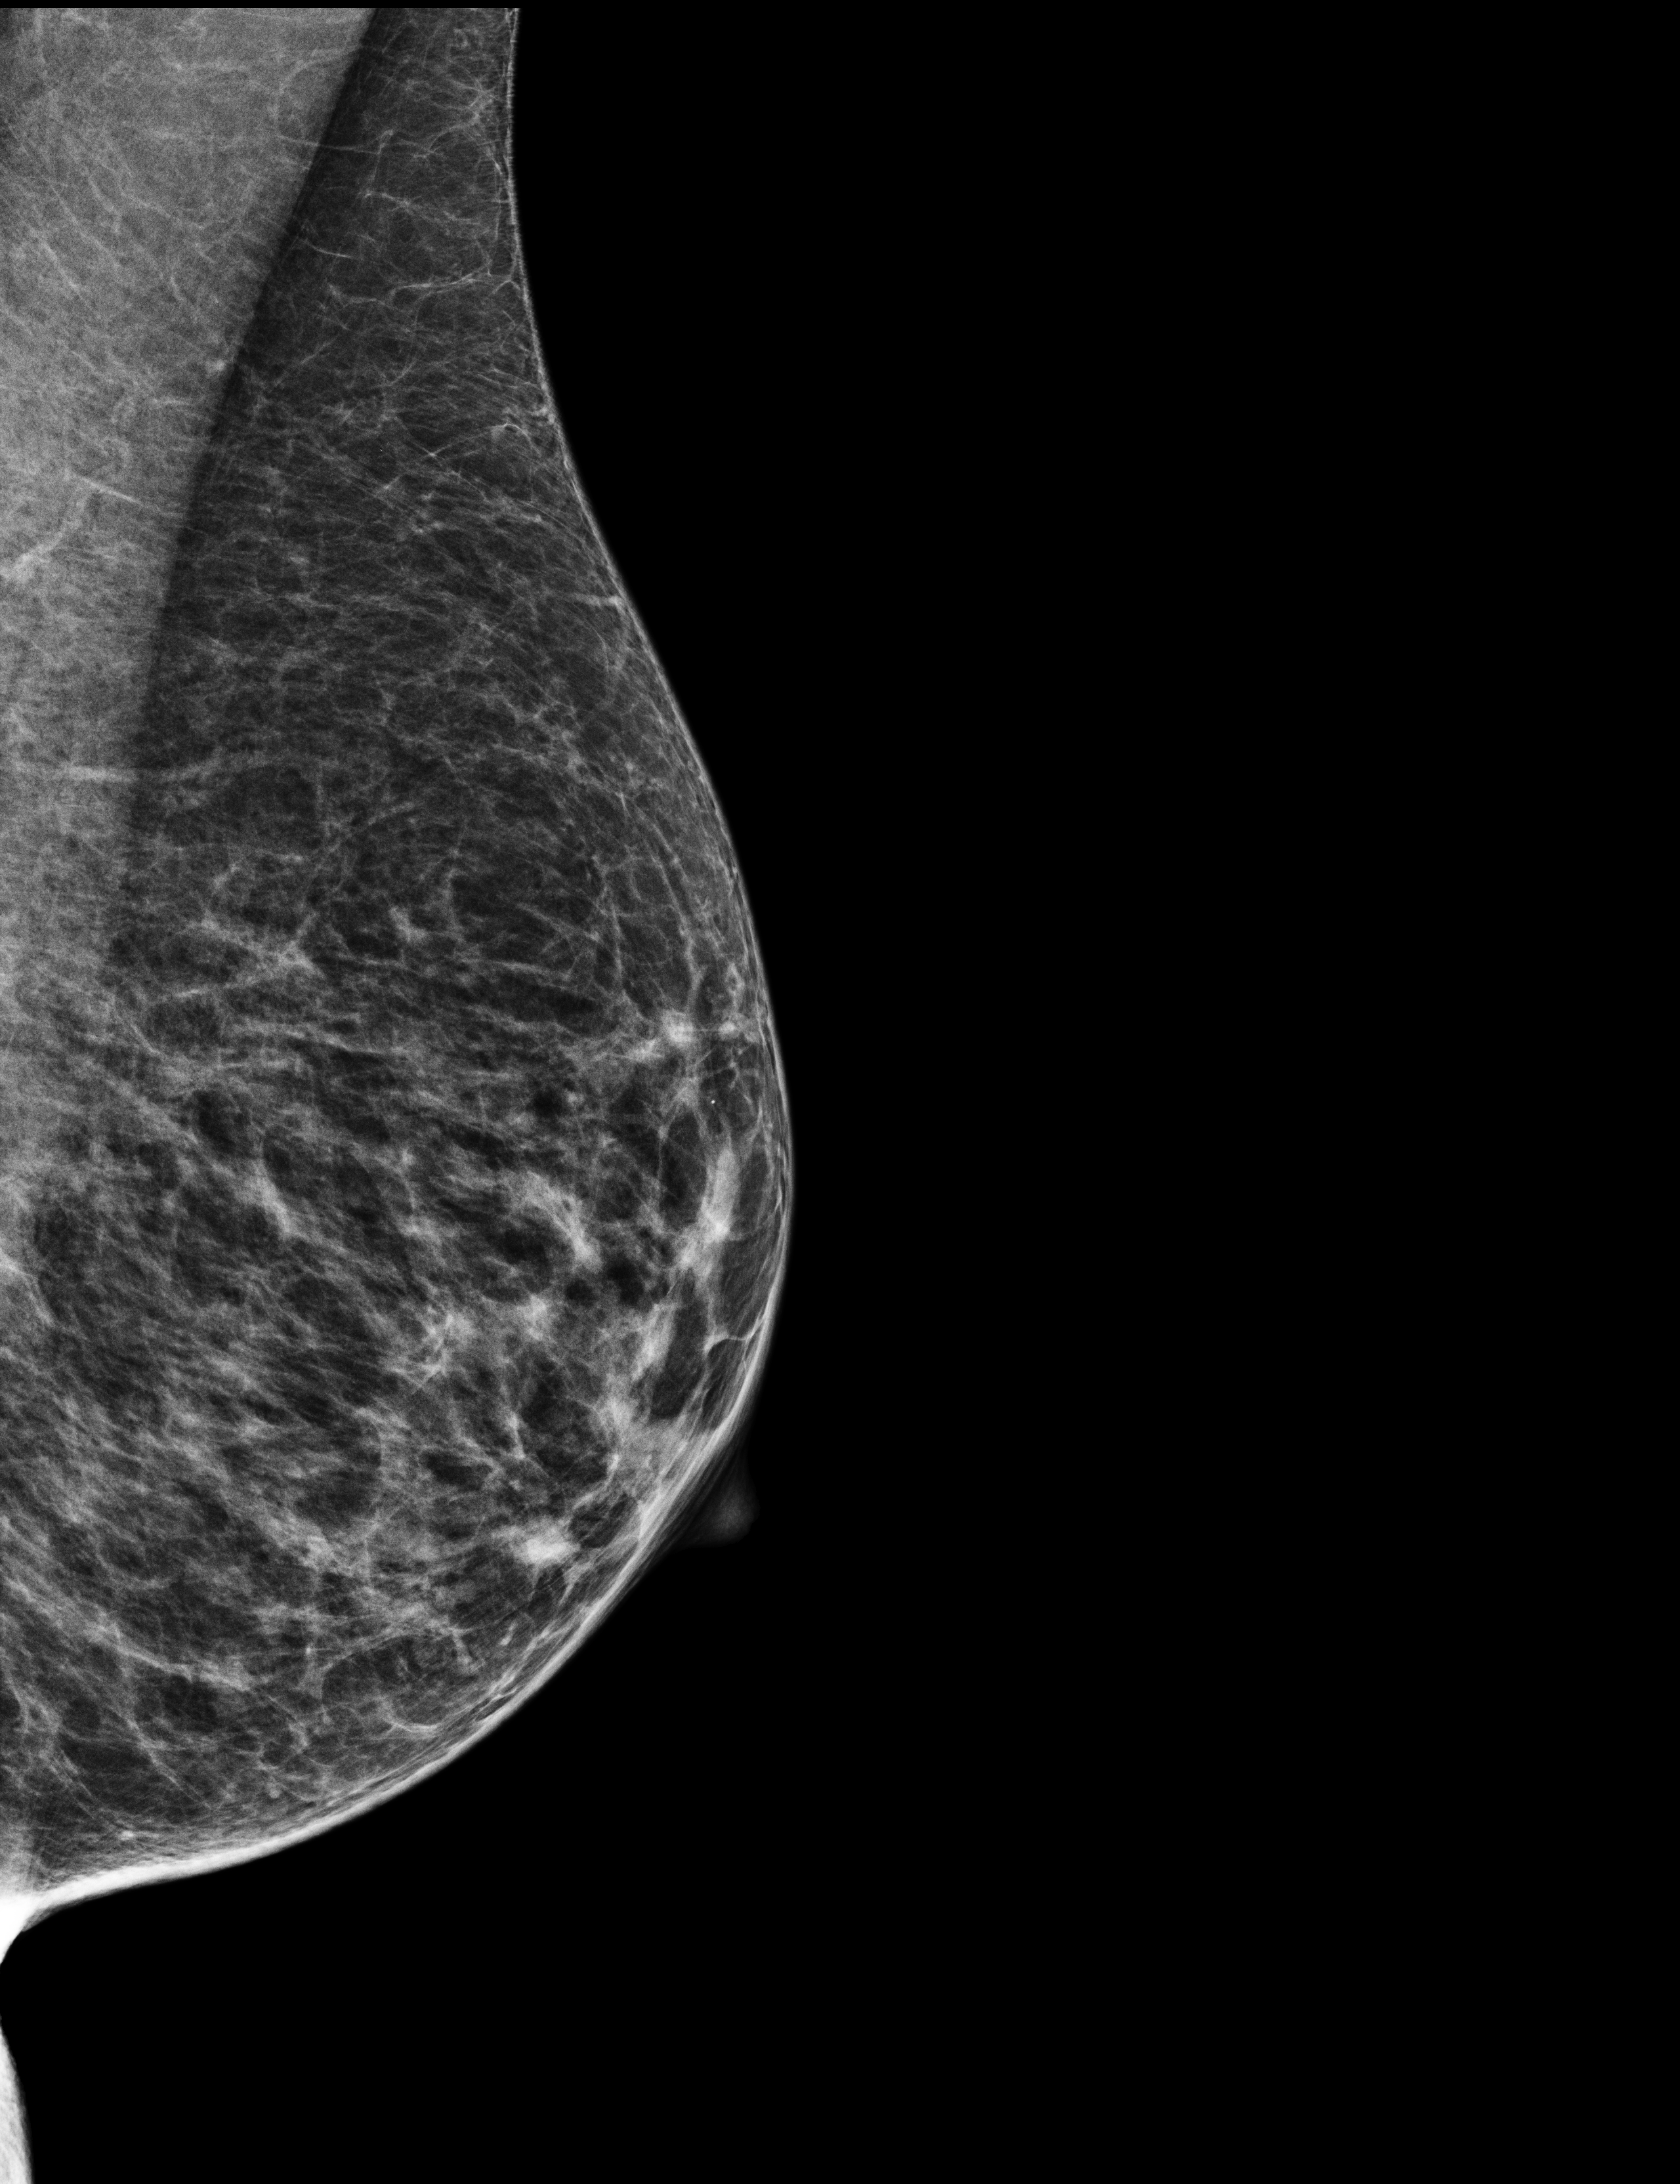
Screening examination.
Image type: full-field digital mammogram. Breast: left. Projection: MLO view.